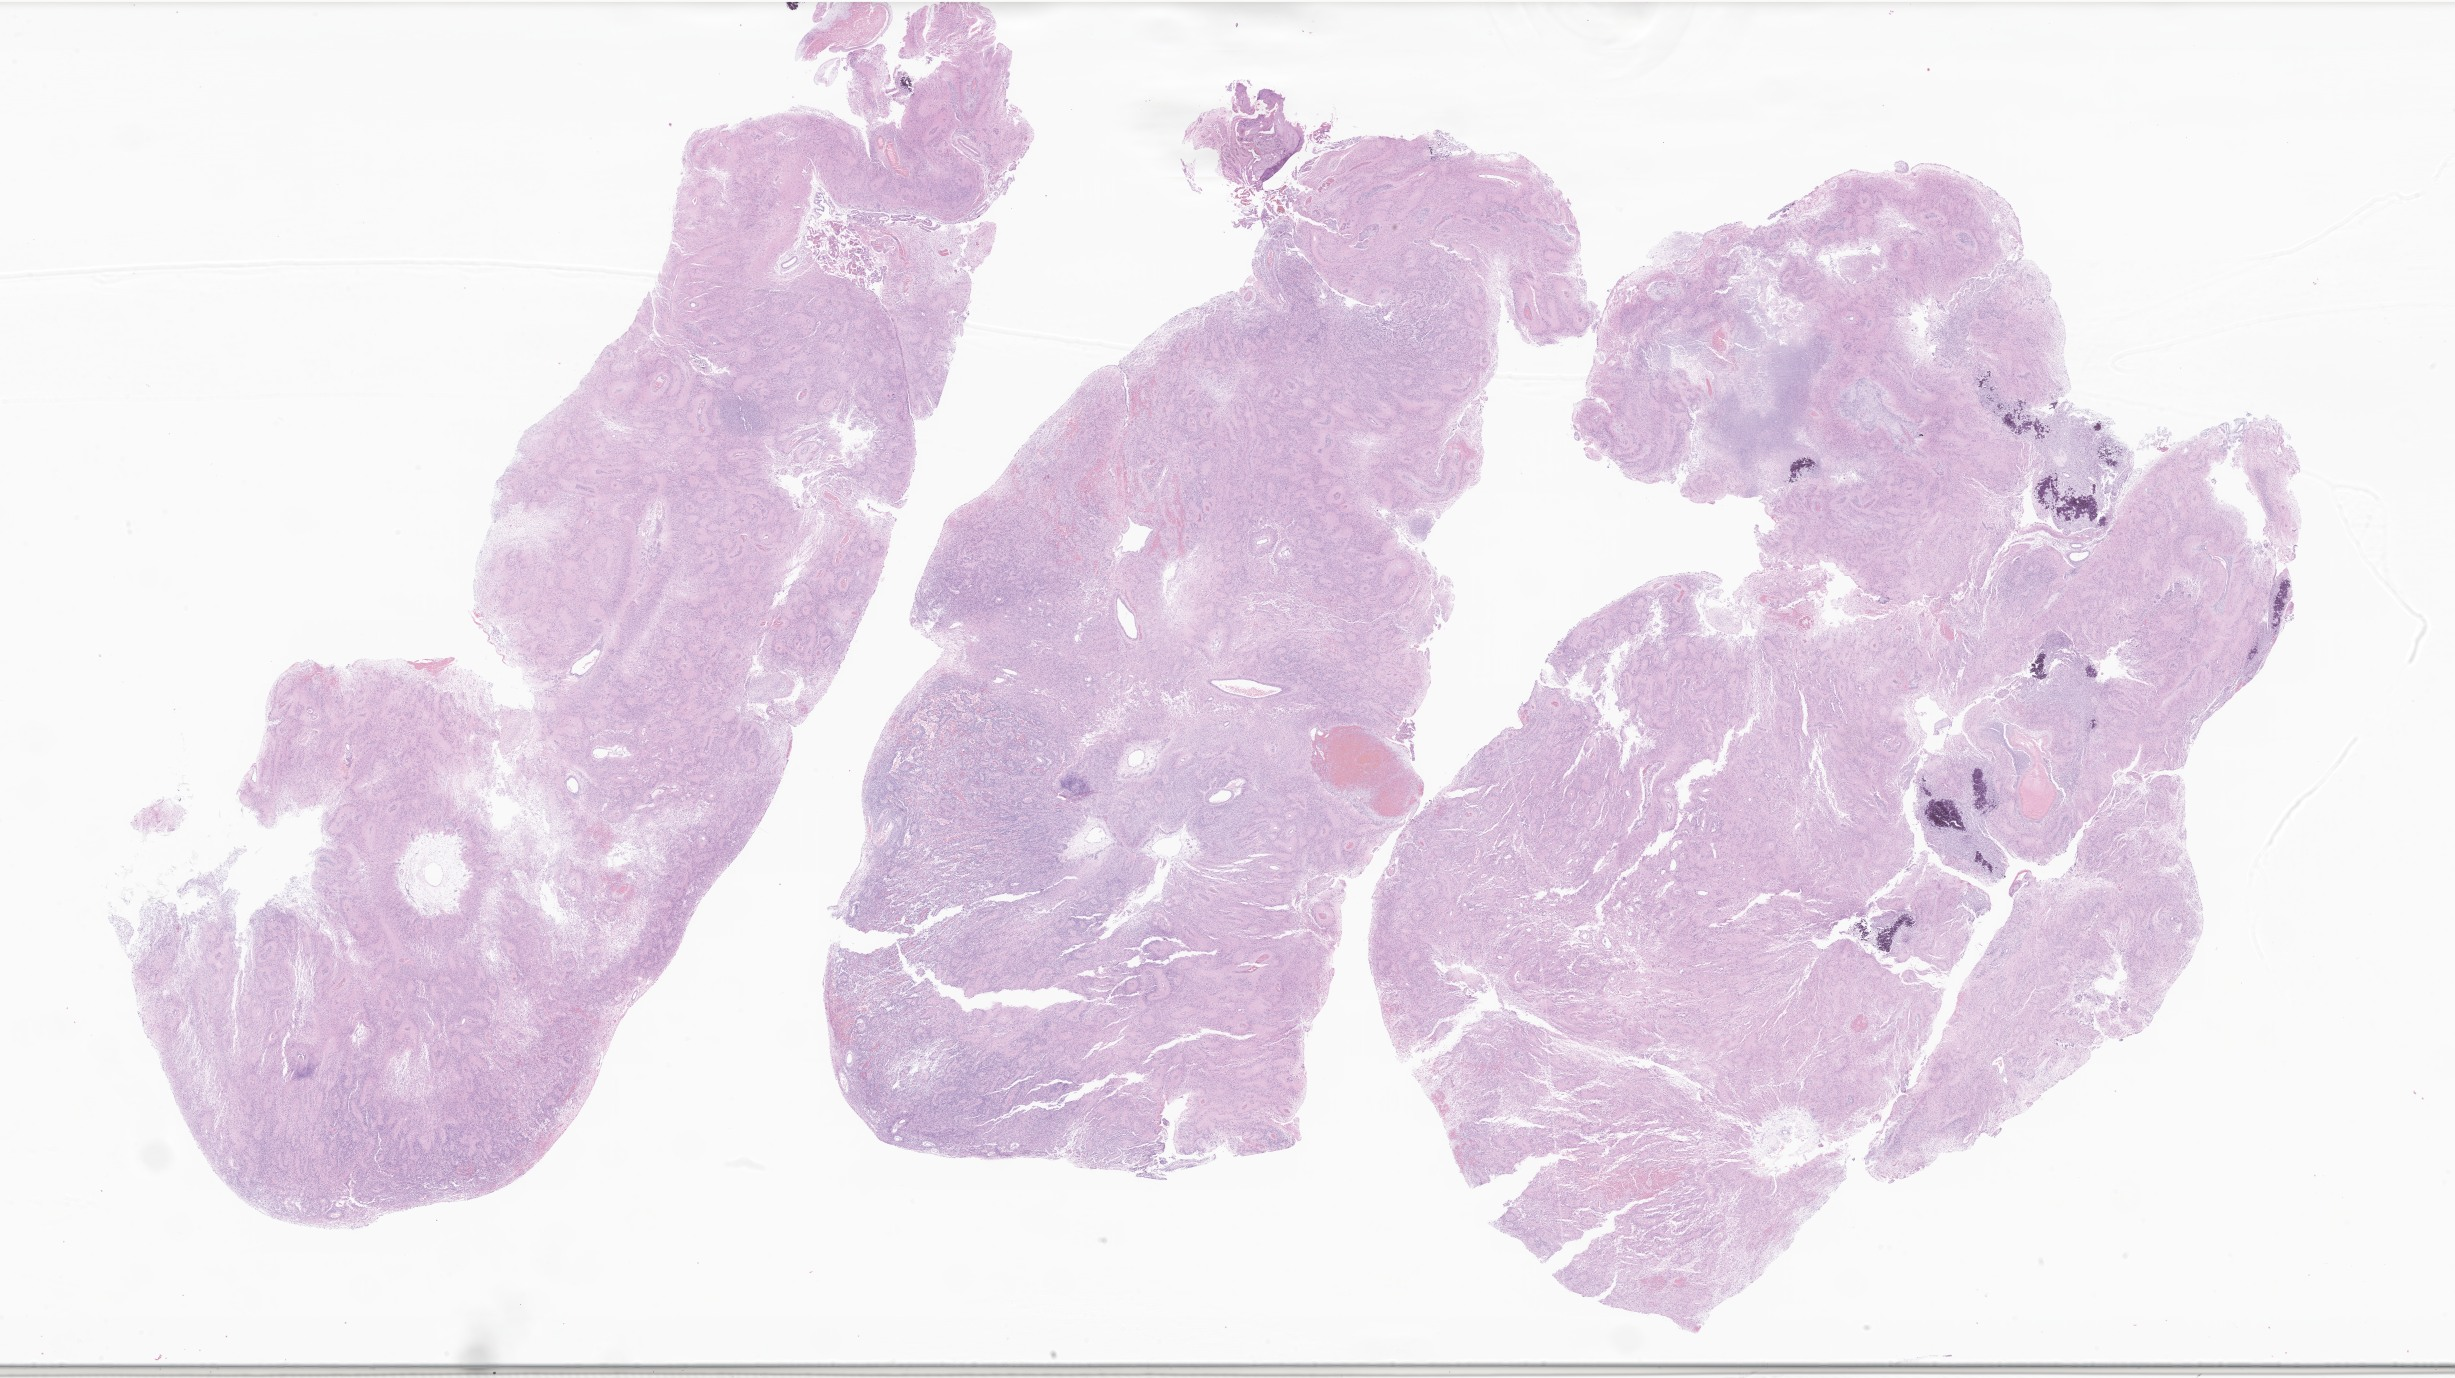
Digitized hematoxylin and eosin (H&E)-stained section of tumor tissue from the cerebellum, low-resolution overview of the scanned area, about 41.4 x 23.2 mm, formalin-fixed, paraffin-embedded (FFPE) tissue. Patient: male, age 596 days (about 1.6 years).
Diagnosis: Ependymoma, NOS.